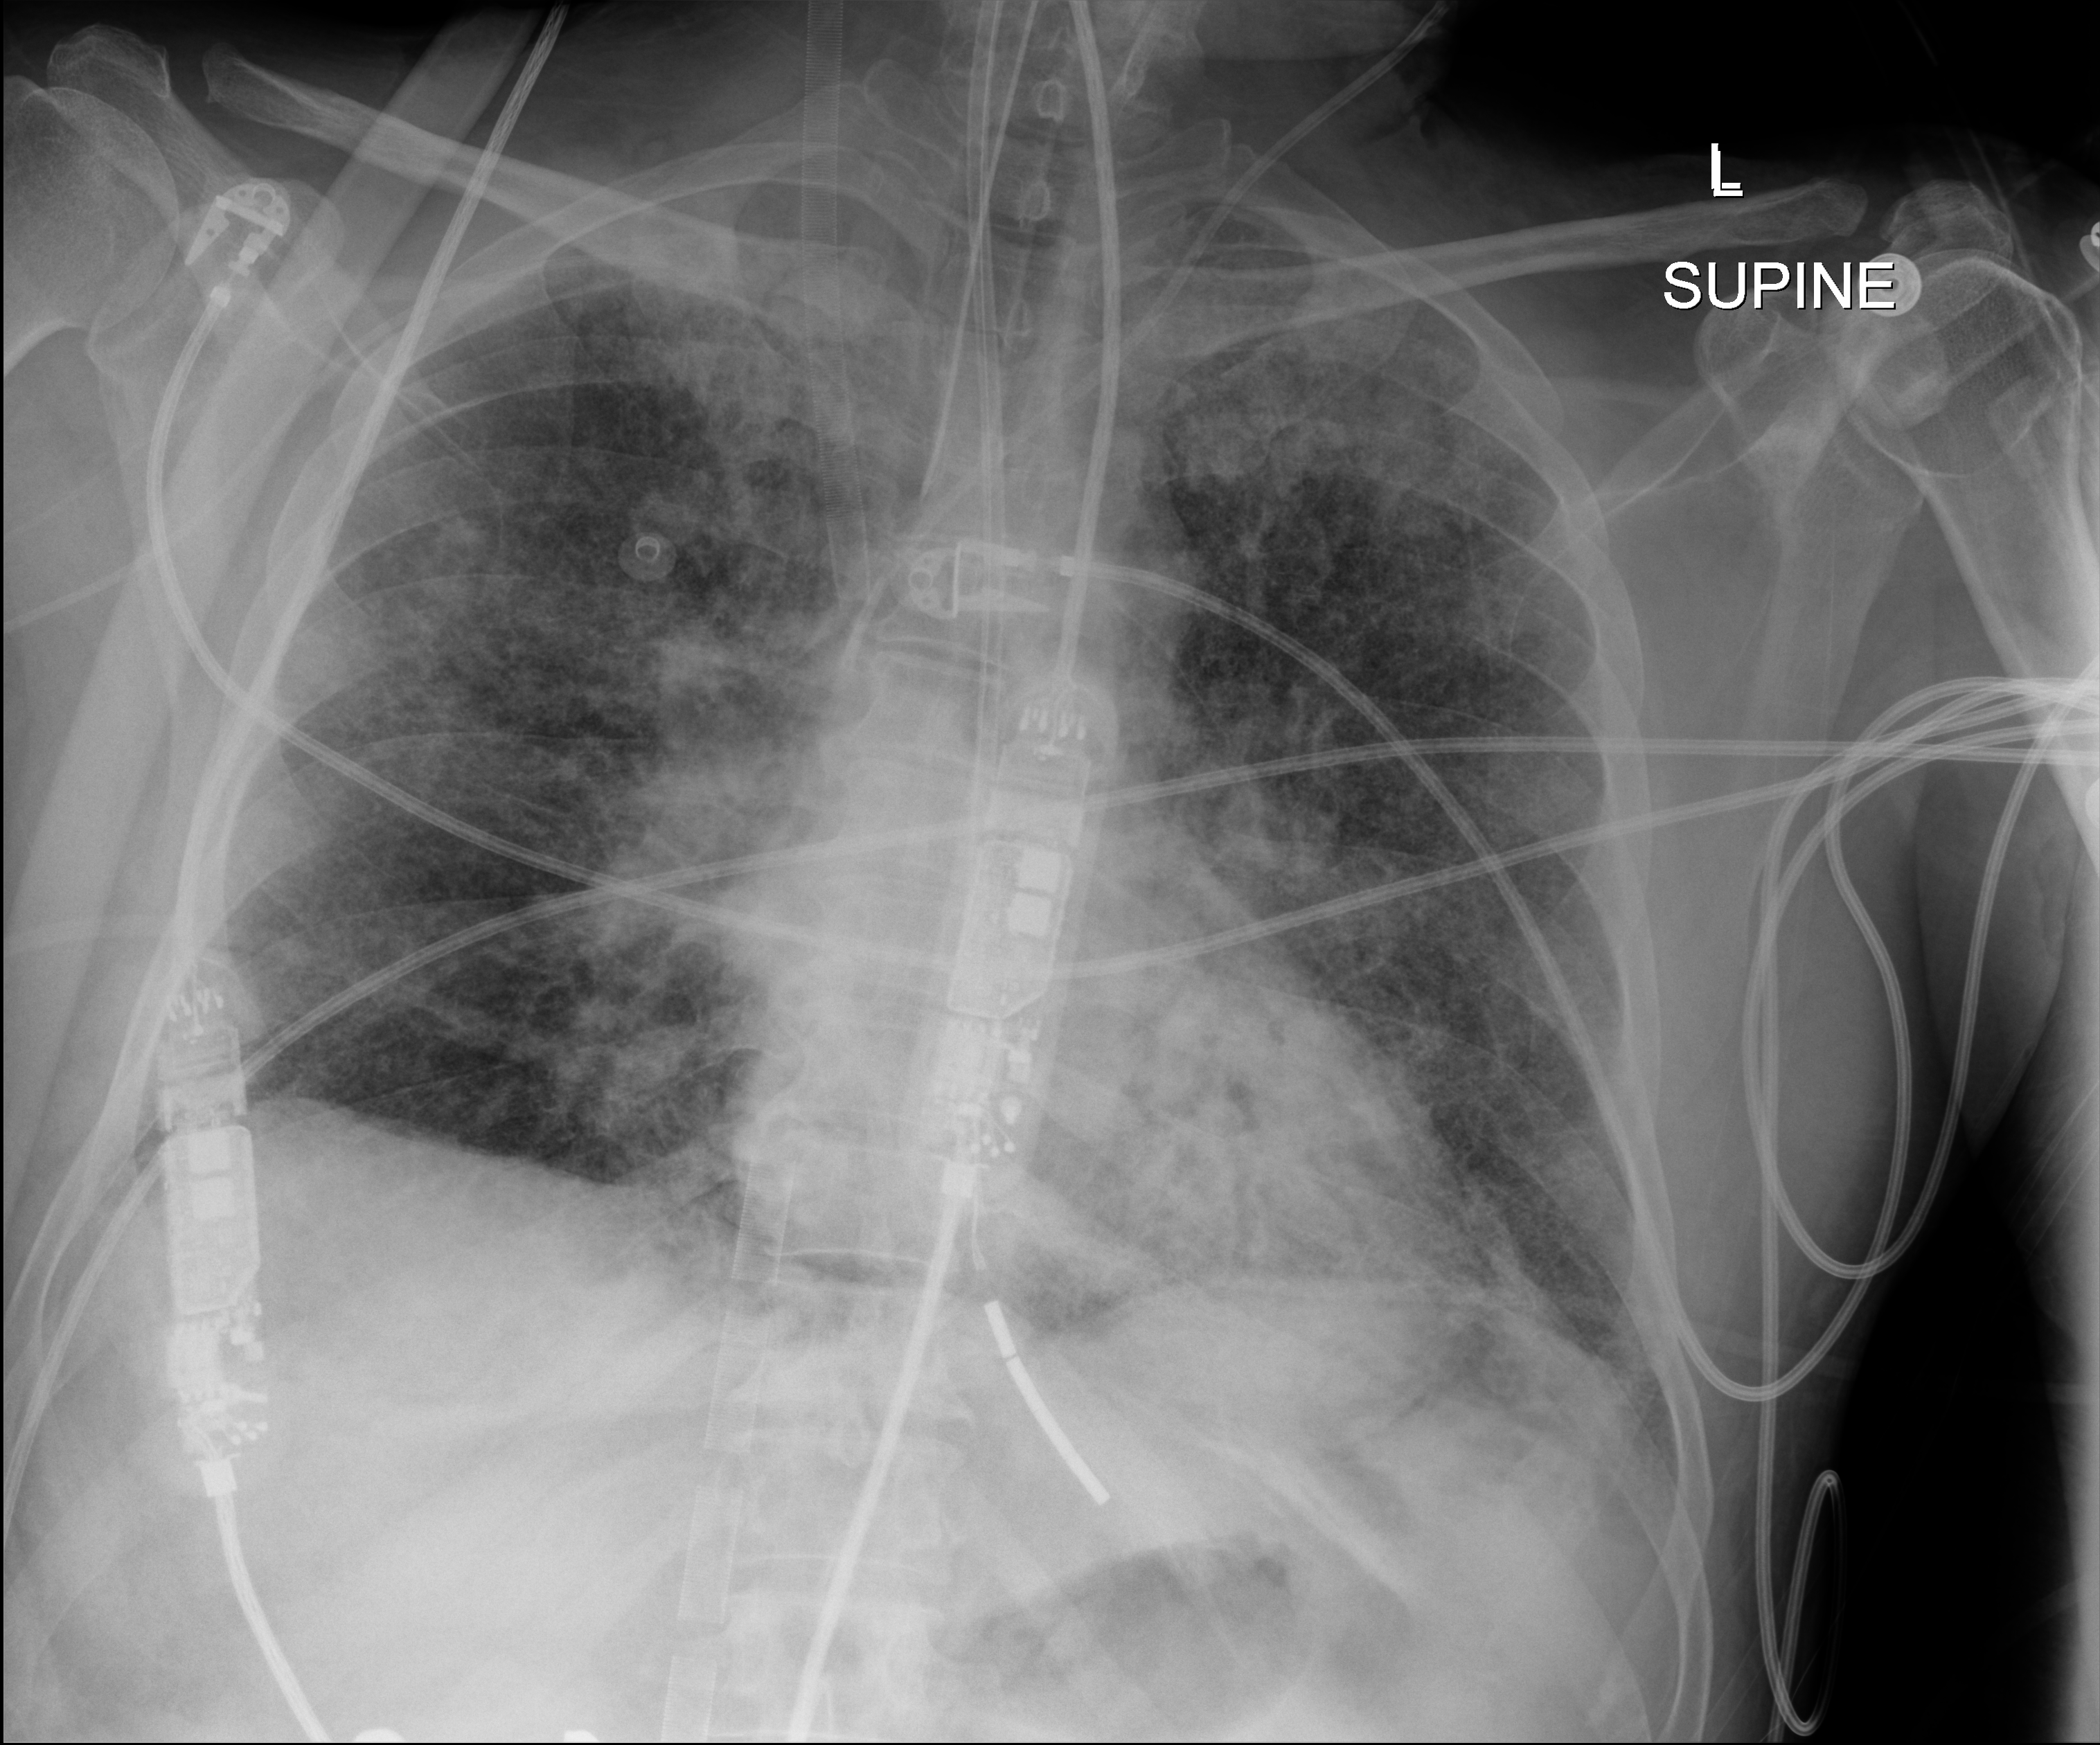
Bedside chest radiograph (digital radiography); anteroposterior (AP) projection. Male patient hospitalised with COVID-19, age 18–59 years.
From the hospital-stay record, not from the radiograph (when in the stay this image was taken is not recorded): hypertension (admission record): no; diabetes (admission record): no.